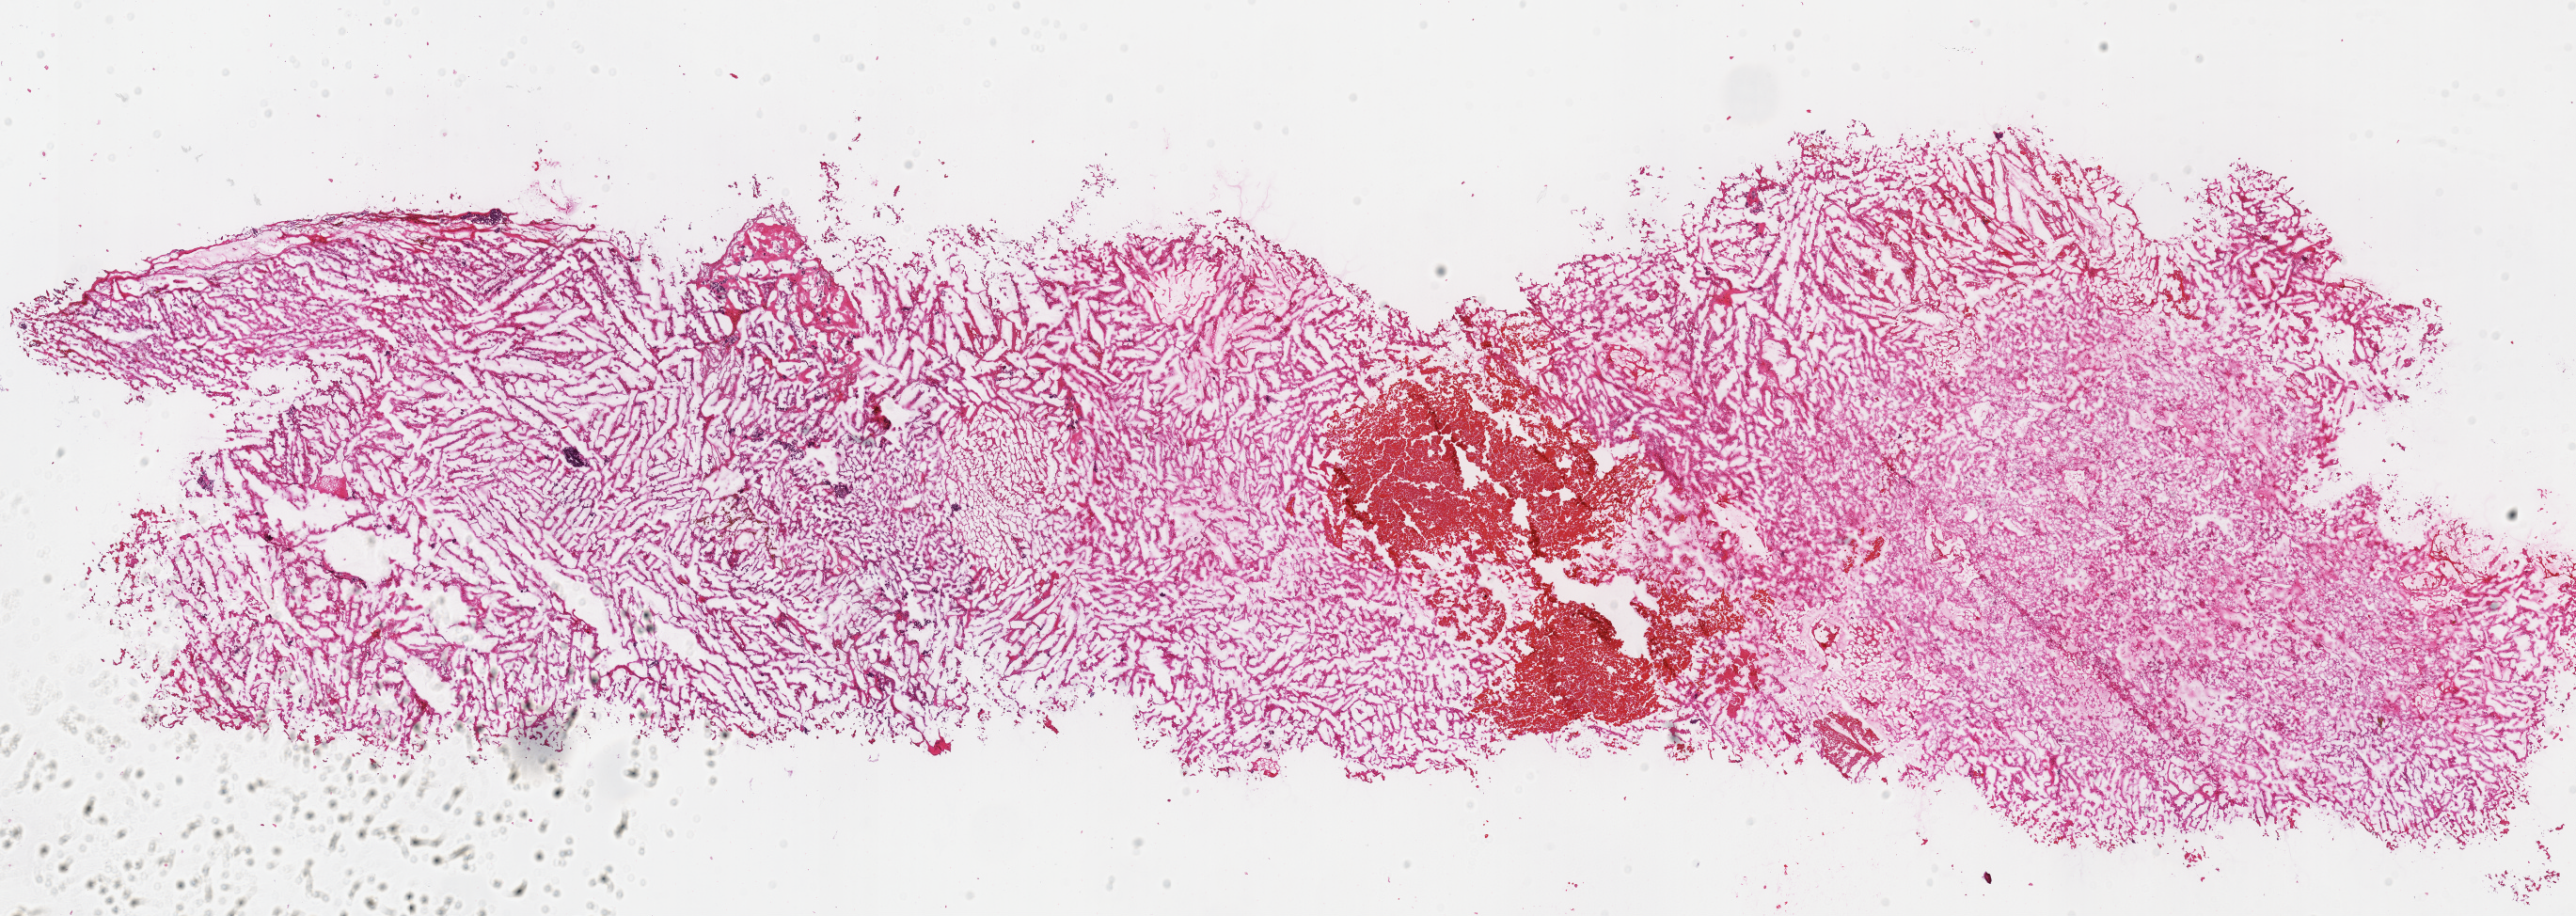
Whole-slide histology image, H&E — shown as a low-resolution overview of the whole scanned area (about 21.5 x 7.7 mm), frozen section from the top of the tissue portion, sample: primary tumour, kidney. Male, age 41 years at initial diagnosis.
Histologic diagnosis: Renal cell carcinoma, chromophobe type.